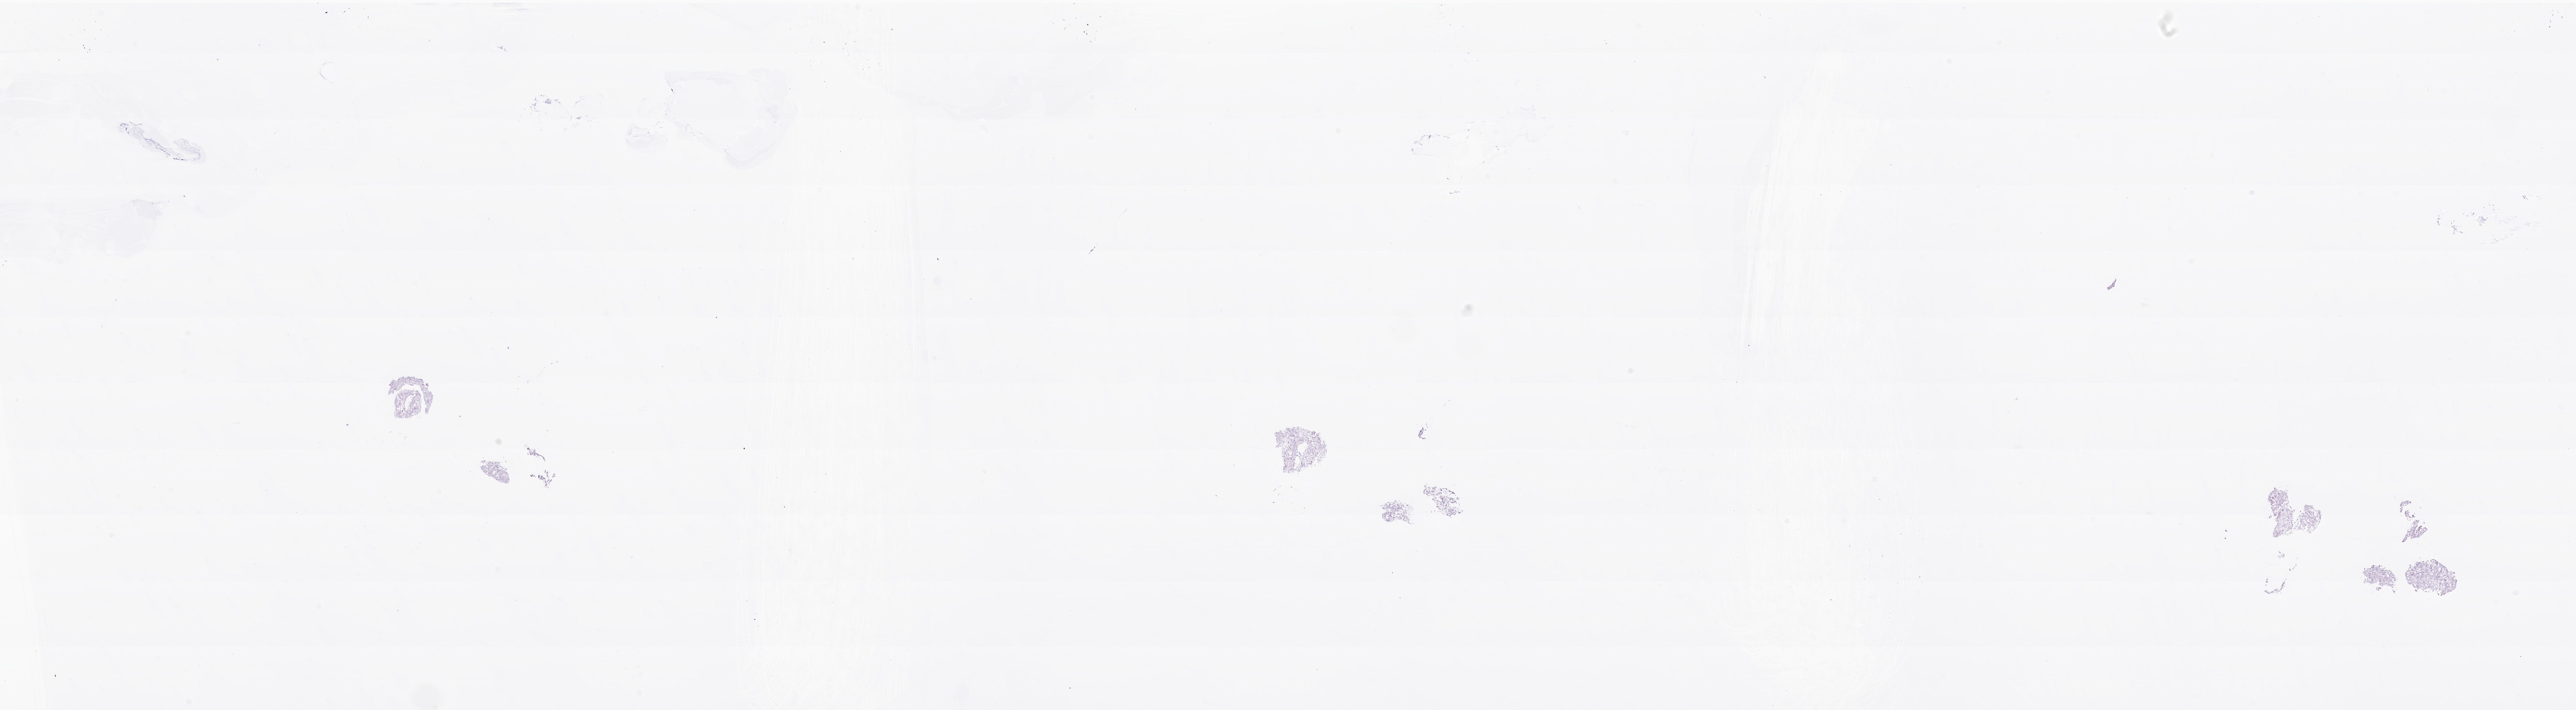
Hematoxylin and eosin (H&E) whole-slide image of tumor tissue from the cerebellum — a low-resolution overview of the entire scanned area, about 41.6 x 11.5 mm, cryosection (OCT / tissue freezing medium). Female patient, age 44 months (3 years 8 months).
* recorded diagnosis: Oligoastrocytoma, NOS